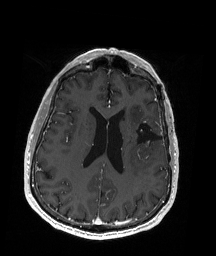
Brain MRI from a brain-tumour surgery series, one axial slice. Position 78 of 192 along the scan axis. T1-weighted post-contrast. 1 mm slice thickness. 216 × 256 image matrix, field of view 211 × 250 mm. Case-level facts recorded for this patient, not image findings: histopathology: Oligodendroglioma; WHO grade: 2; IDH mutation: yes; tumour location: Left Insular.
Structures marked on this image (expert manual segmentation):
- previous resection cavity: bounding box <132,121,163,148> (left, top, right, bottom; pixels)